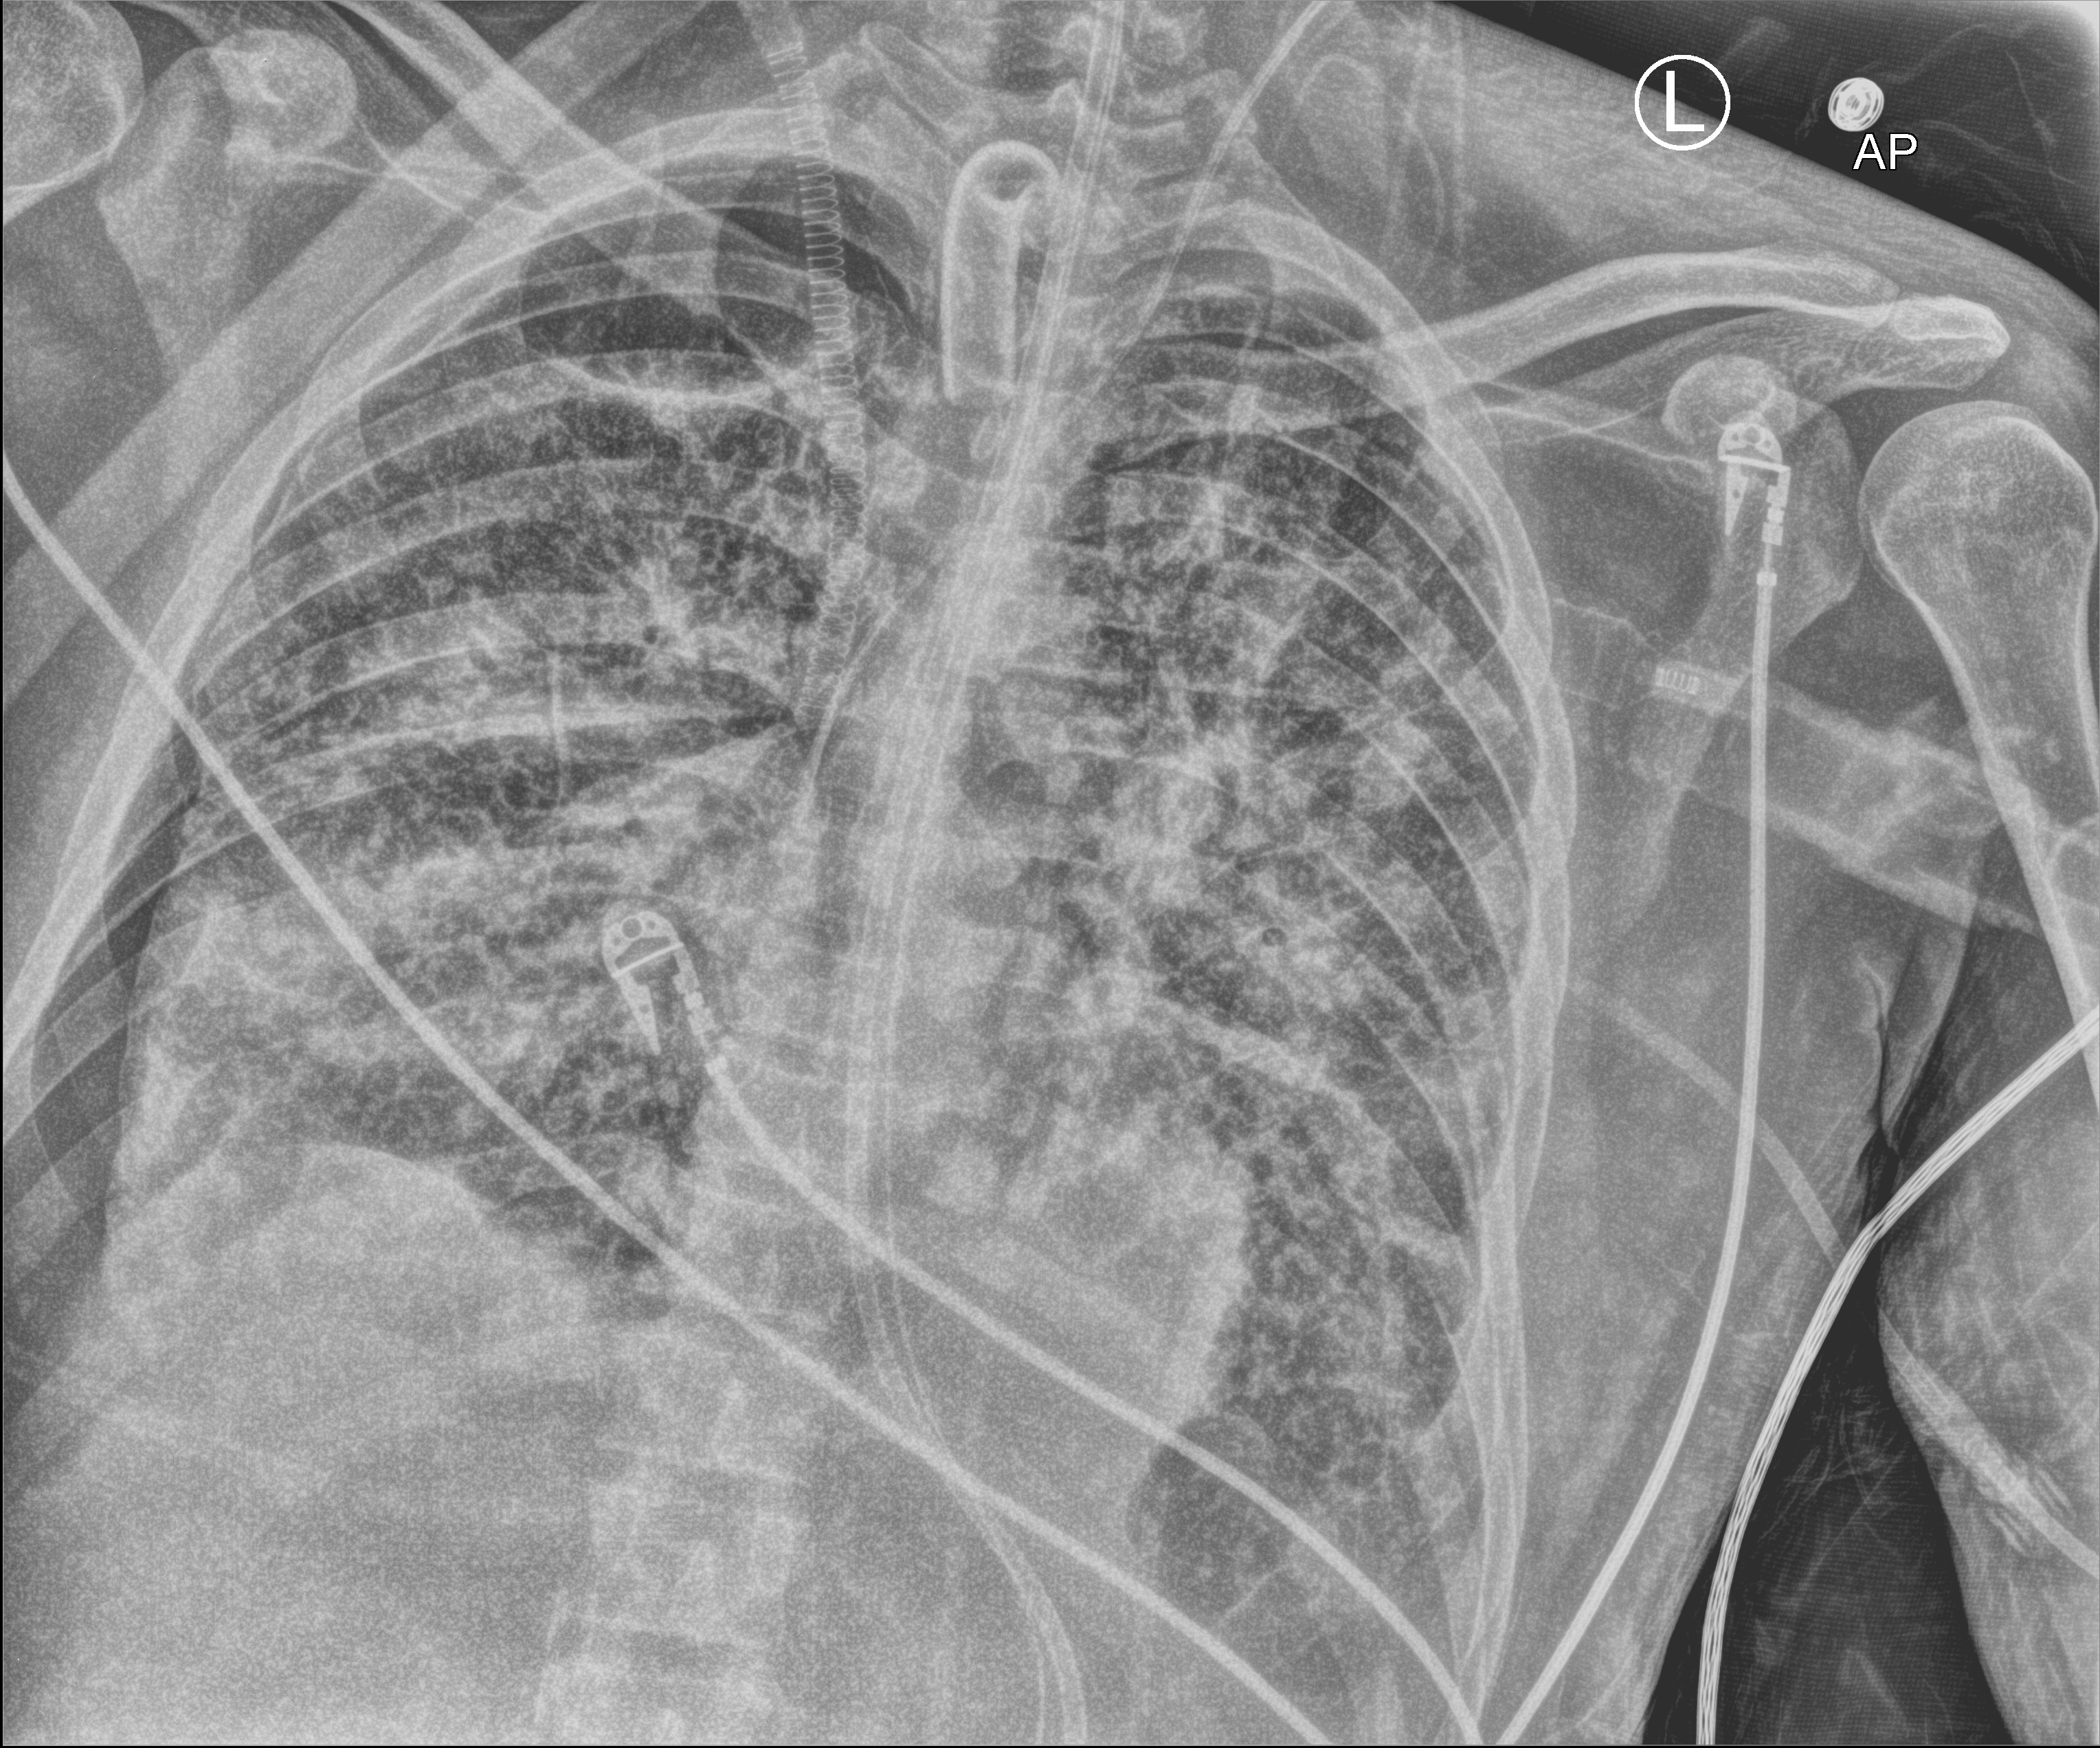
Portable chest radiograph, anteroposterior (AP) projection. Adult patient hospitalised with COVID-19, age 18–59 years.
Admission-level facts for this patient (not findings on this image; timing relative to this image not recorded): mechanically ventilated during this hospital stay: yes.